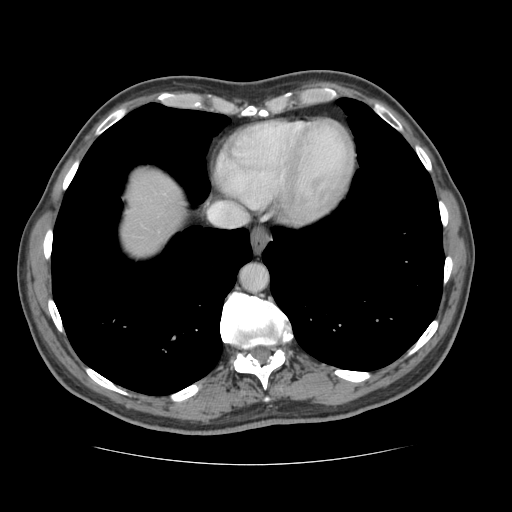
Contrast-enhanced abdominal CT, one axial slice. Position 121 of 134 along the scan axis. Reconstruction kernel STANDARD. Intravenous contrast given. Soft-tissue window (W 400 / L 40 HU). 512 × 512 image matrix, field of view 377 × 377 mm. Male patient, age 68 years. Case-level facts recorded for this patient, not image findings: diagnosis: colorectal cancer liver metastases, imaged before liver resection; multiple liver metastases: yes; largest metastasis: 2.2 cm; chemotherapy before resection: no.
Annotated regions visible in this slice (outlined manually by an expert reader):
- hepatic veins: bounding box <227,205,241,214> (left, top, right, bottom; pixels)
- liver: <123,178,175,240>
- planned liver remnant (the part of the liver to remain after resection): <123,177,174,240>